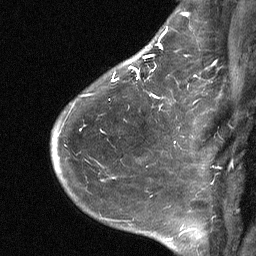
Breast MRI (dynamic contrast-enhanced), one sagittal slice. Position 48 of 64 along the scan axis. Dynamic contrast-enhanced study with each time point stored as its own series, time point 2 of 3 at this slice position (early post-contrast, ordered by acquisition time). 1.5 T. TE 4.8 ms, TR 27 ms. 2 mm slice thickness. 256 × 256 image matrix, field of view 180 × 180 mm. Patient: female, 51 years. Case-level facts recorded for this patient, not image findings: setting: breast cancer imaged before/during neoadjuvant chemotherapy; receptor status: HR-positive, HER2-negative.
Annotated regions visible in this slice (semi-automatic segmentation, software-assisted and operator-edited):
- analysis volume of interest (the breast-tissue region the enhancement analysis was run in; not a lesion): bounding box [x1, y1, x2, y2] px = [72, 34, 182, 118]
- tumour enhancement mask (voxels above the 90 % enhancement threshold inside the analysis volume of interest): [112, 34, 163, 99]